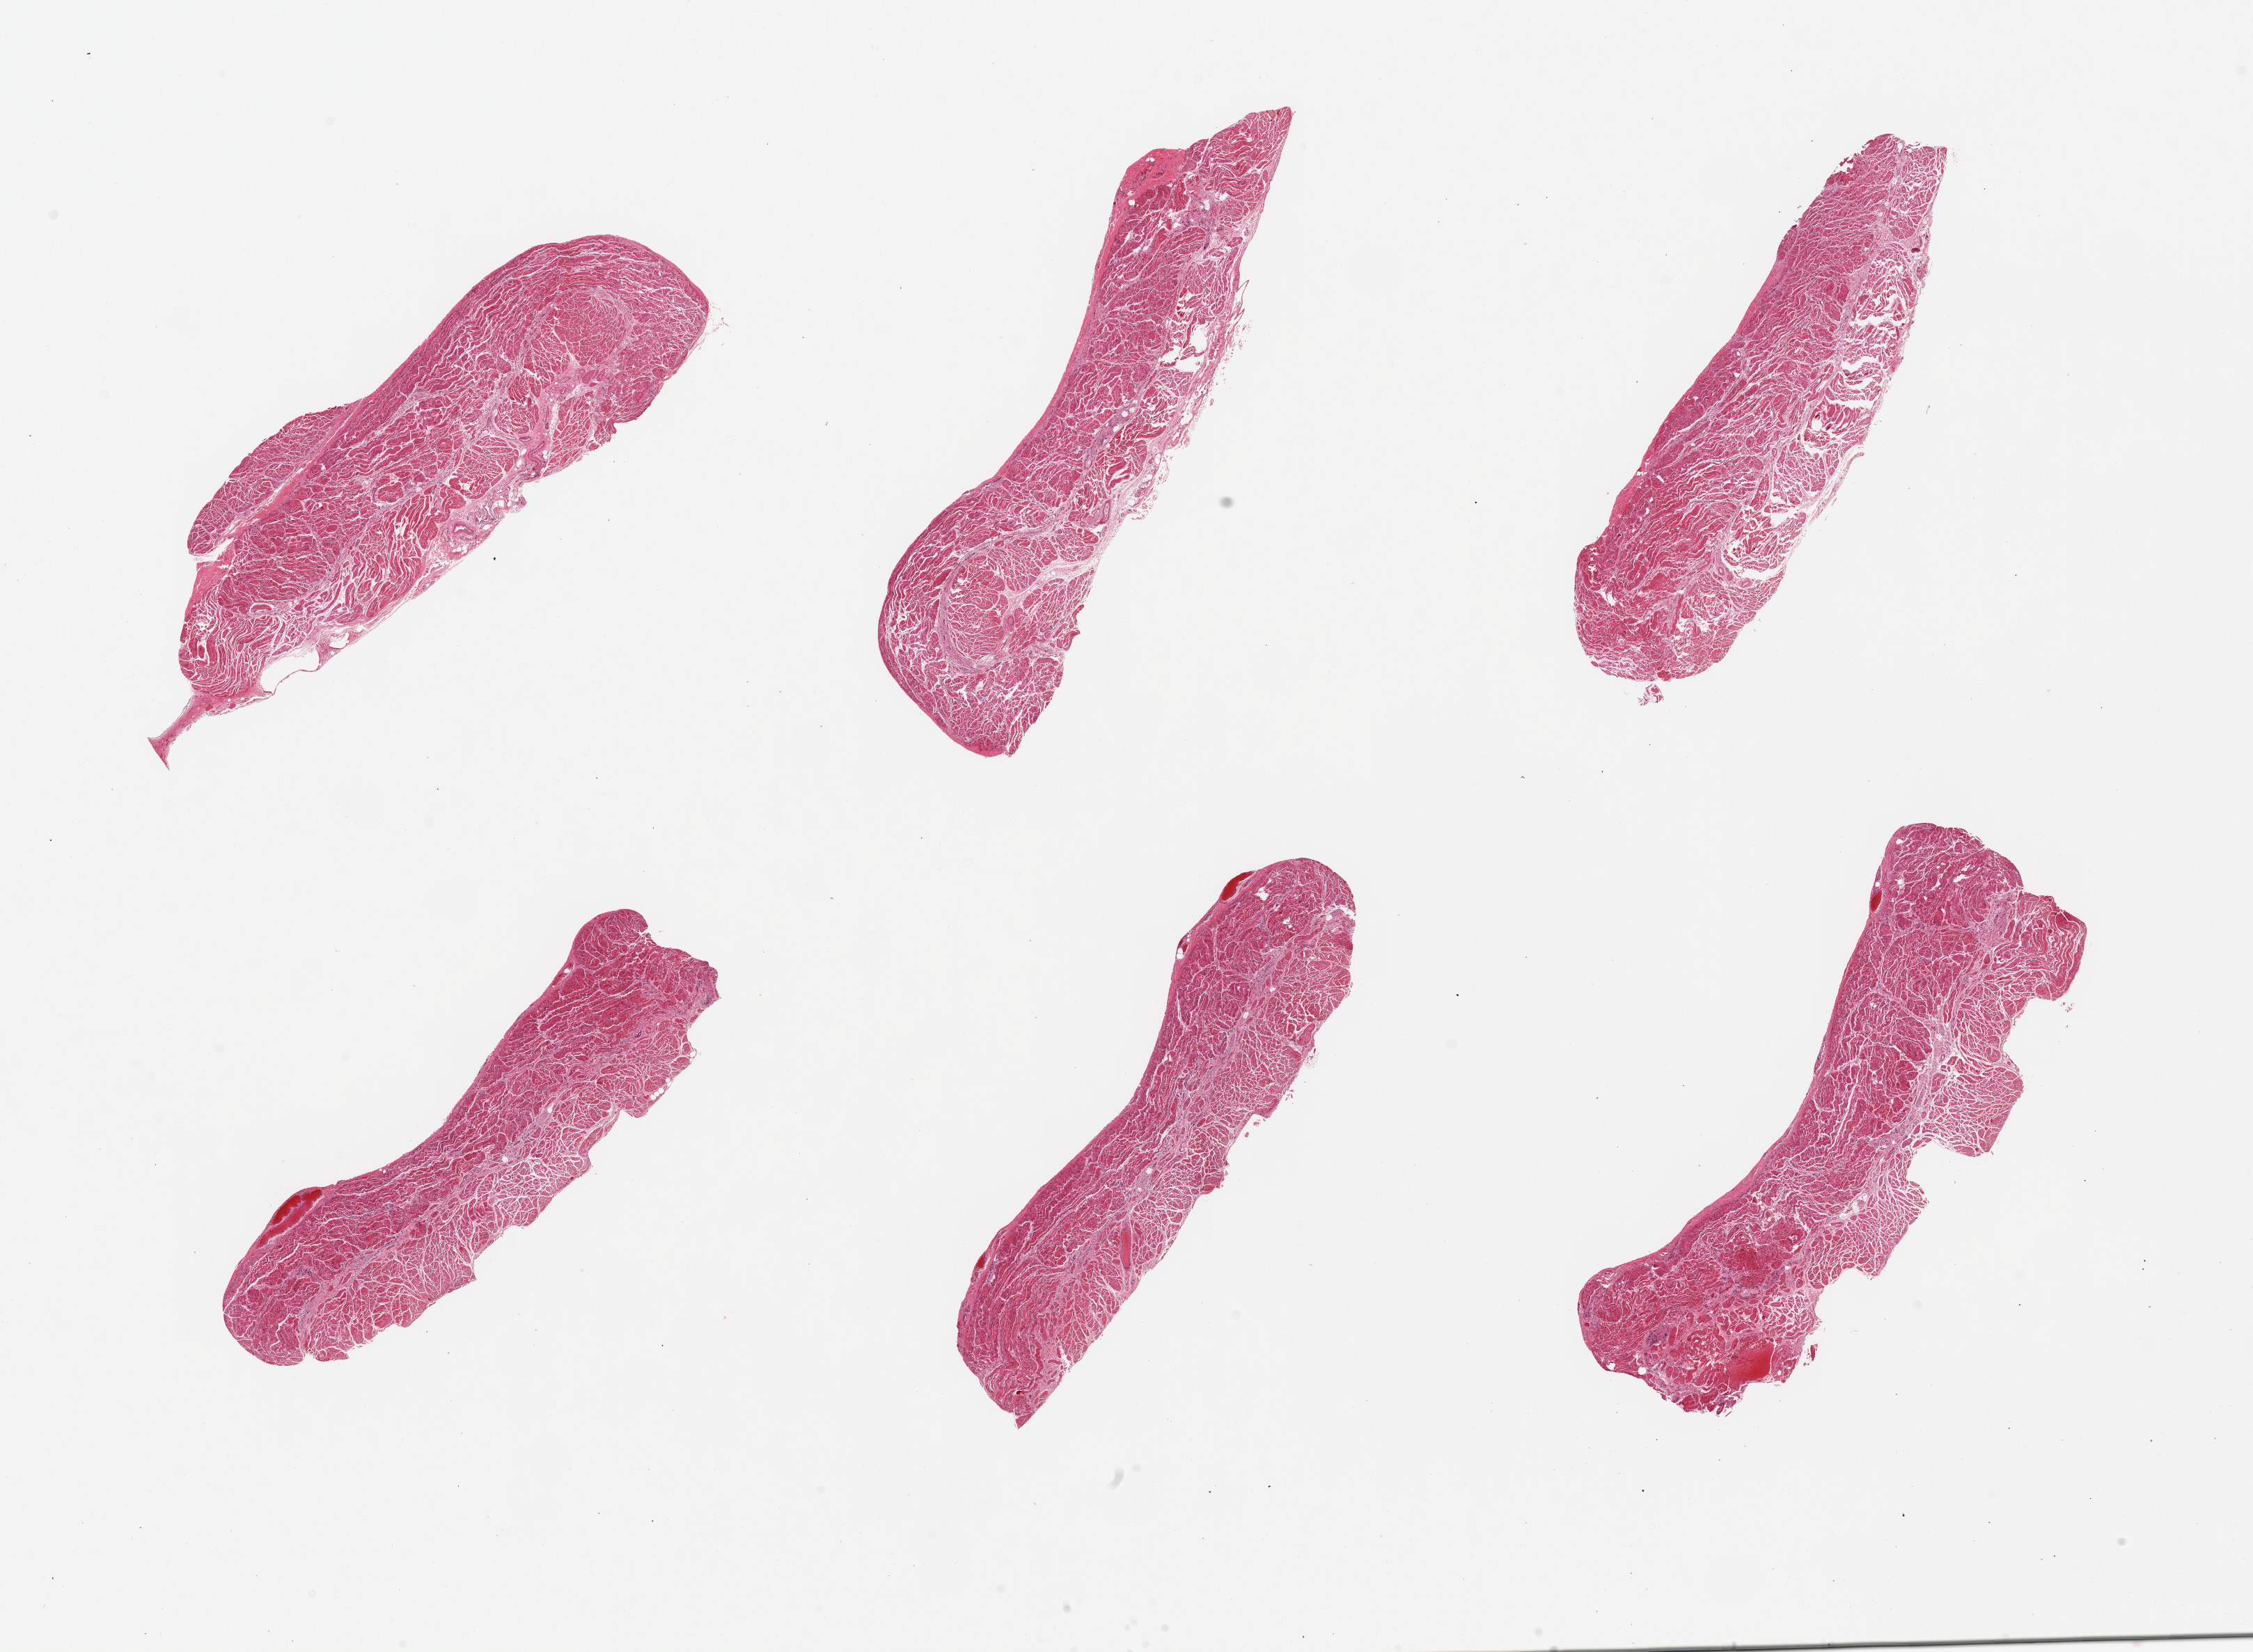
Whole-slide image, H&E stain, brightfield — low-resolution overview of the scanned area, about 25.6 x 18.8 mm, PAXgene-fixed paraffin-embedded (PFPE) section, target tissue: gastroesophageal junction, donor tissue sample. Donor: male.
* pathologist's review note for this sample: 6 pieces; well dissected